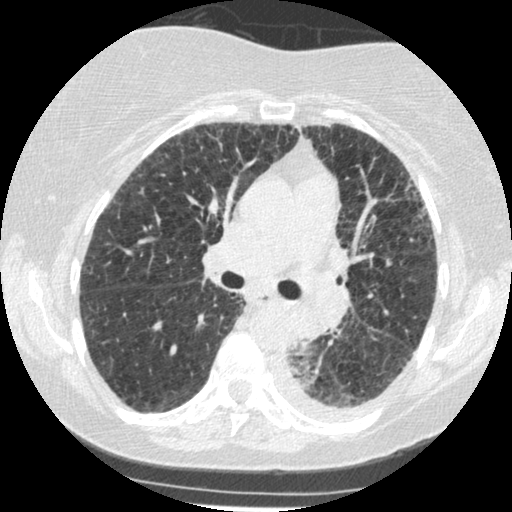
Low-dose screening chest CT, one axial slice. Position 159 of 341 along the scan axis. Reconstruction kernel STANDARD. Lung window (W 1500 / L -600 HU). 1.25 mm slice thickness. 512 × 512 image matrix, field of view 310 × 310 mm.
Outlined on this slice (expert manual segmentation):
- lesion 1 (tumor, lower lobe of left lung): bounding box [x1, y1, x2, y2] px = [292, 306, 322, 350]